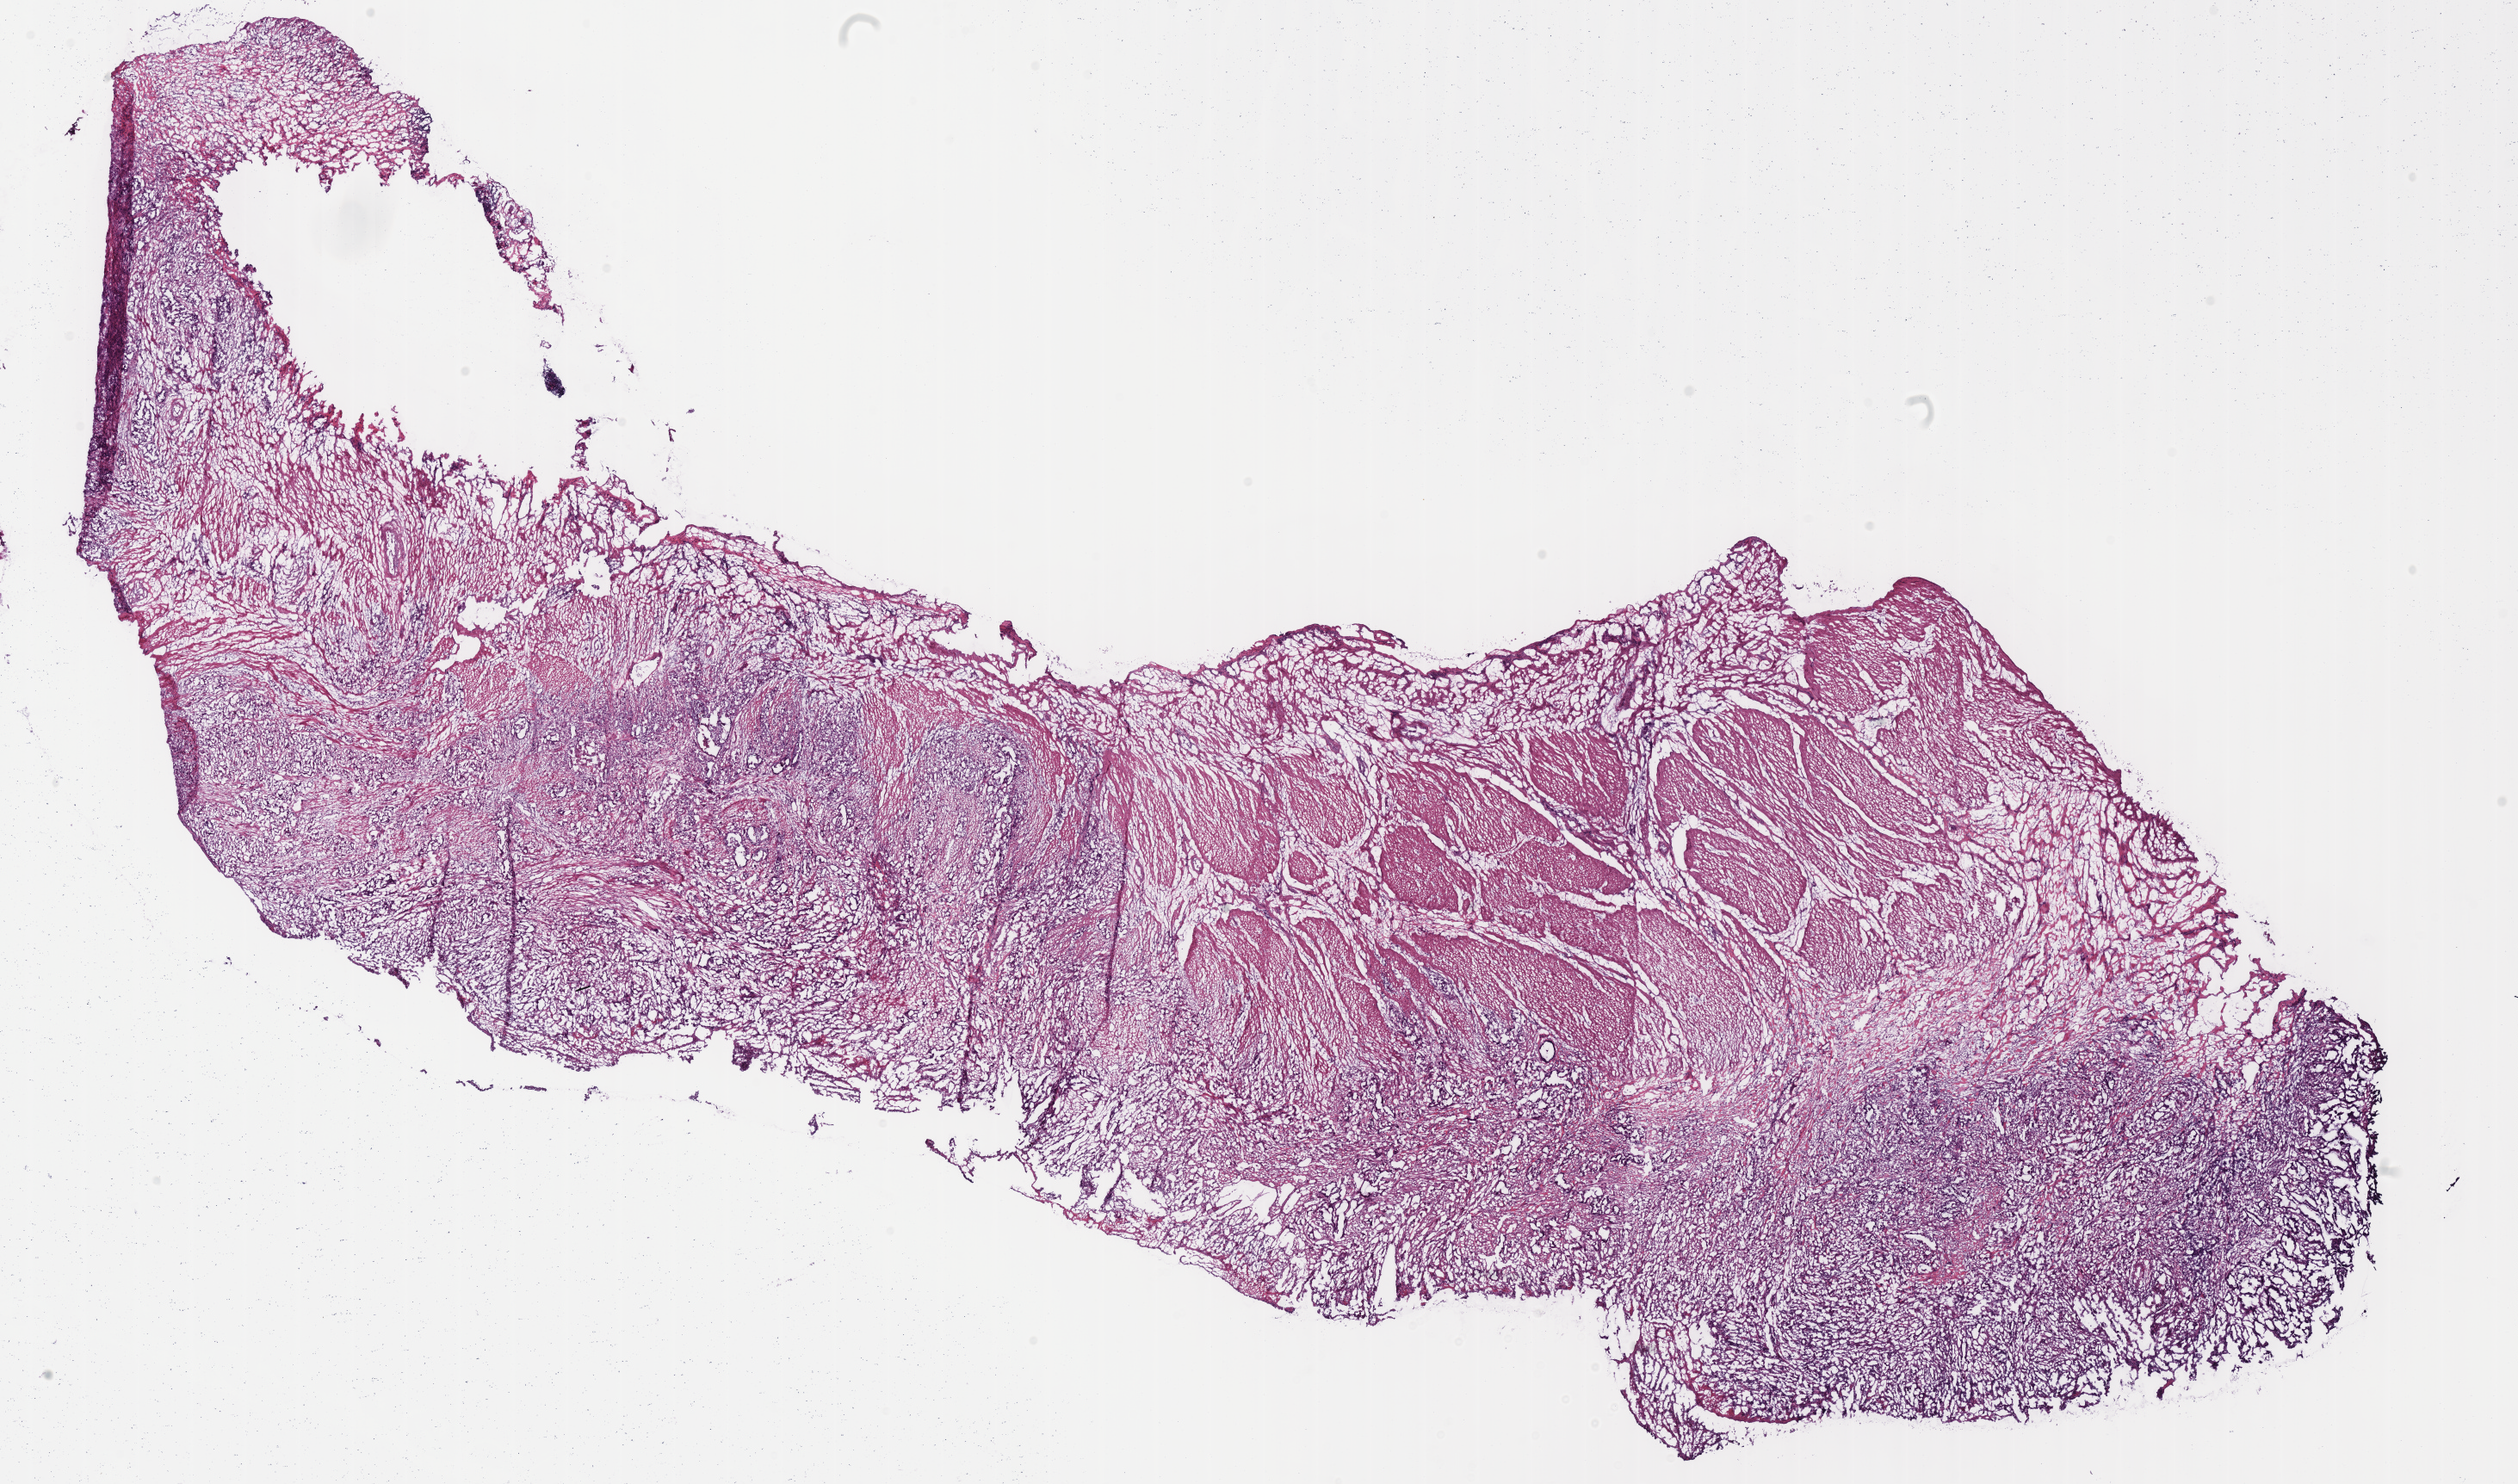
Digitized H&E-stained tissue section (whole slide) — low-resolution overview of the scanned area, about 23.0 x 13.6 mm (slide scanned at 40x); frozen section from the top of the tissue portion; sample: primary tumour, stomach. Patient: male, age at initial diagnosis 72 years. Histologic grade: G3 (poorly differentiated). Slide review estimates, as recorded: tumour cells 60%, tumour nuclei 65%, normal cells 20%, stromal cells 19%, necrosis 1%. Inflammatory infiltration, as recorded: lymphocyte infiltration 5%, monocyte infiltration 2%.
- TNM: T4 N1 M0
- AJCC pathologic stage: III
- diagnosis: Adenocarcinoma, intestinal type (fundus of stomach)